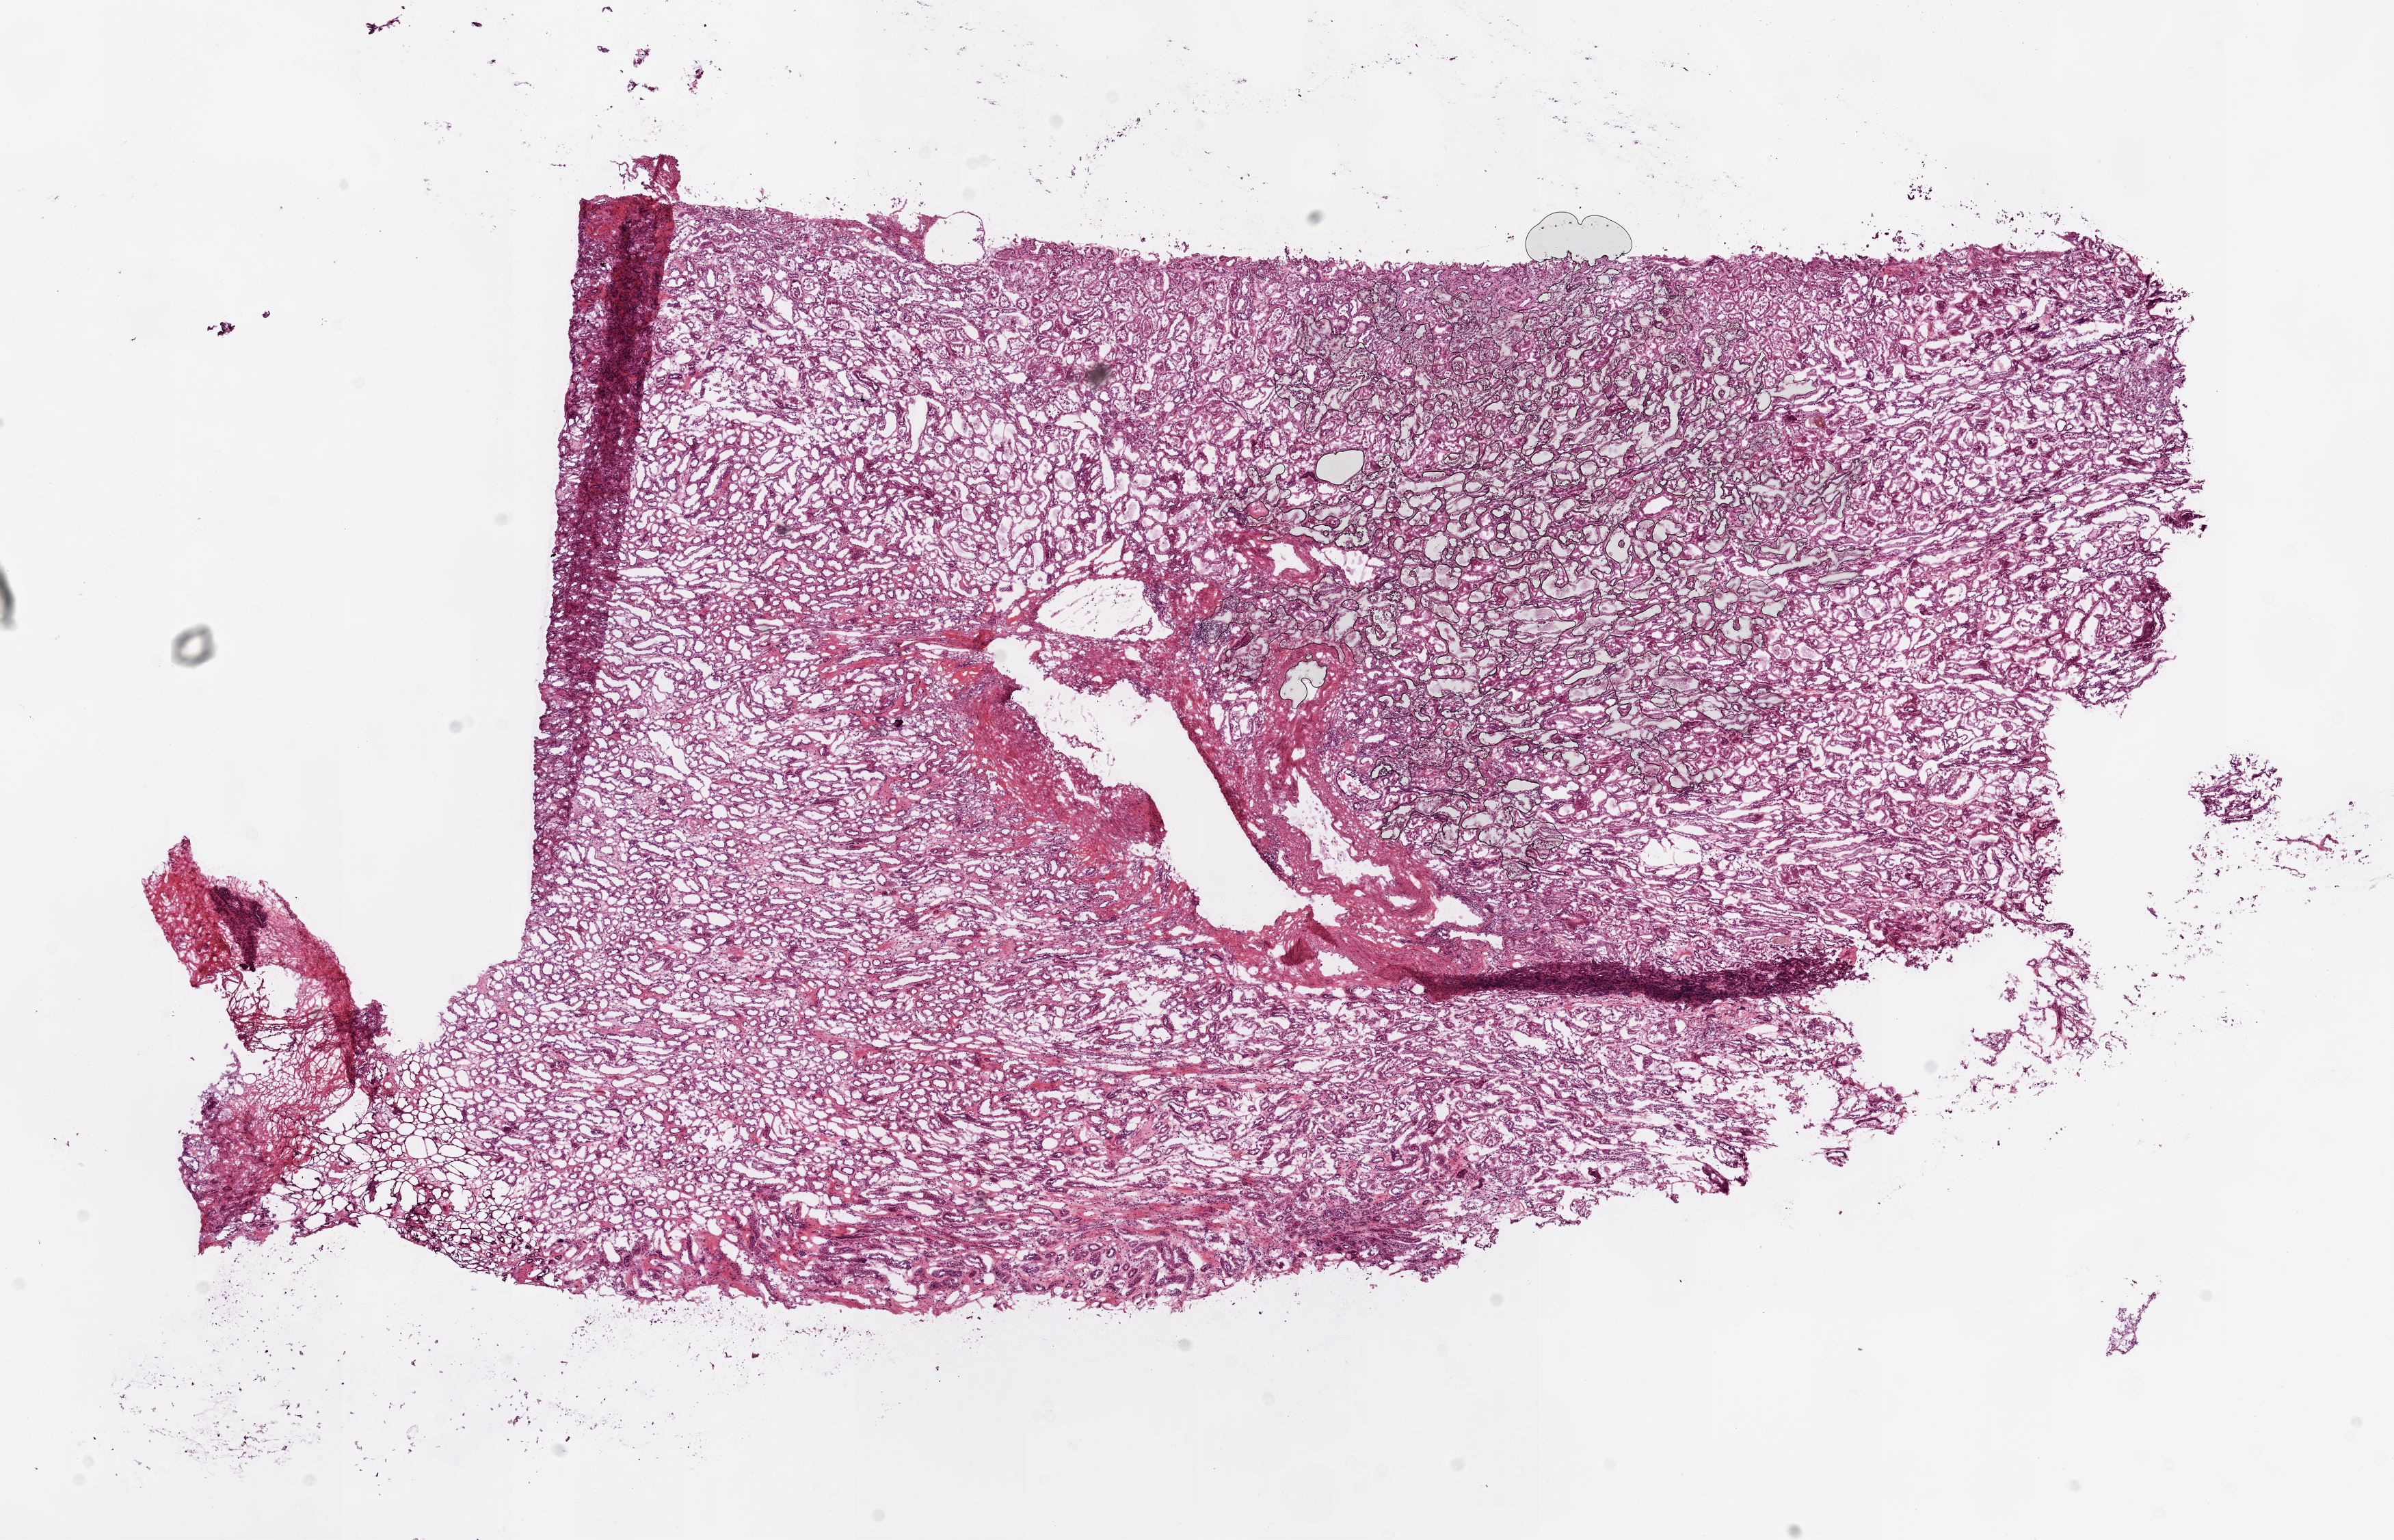
Hematoxylin and eosin (H&E) stained whole-slide image, shown as a low-resolution overview of the whole scanned area (about 13.9 x 8.9 mm, acquisition: 20x scan). Frozen section from the bottom of the tissue portion. Sample: solid tissue normal (non-tumour tissue), kidney. Female, age 46 years at initial diagnosis.
• this section: solid tissue normal (non-tumour) sample from the same patient
• patient diagnosis: Clear cell adenocarcinoma, NOS